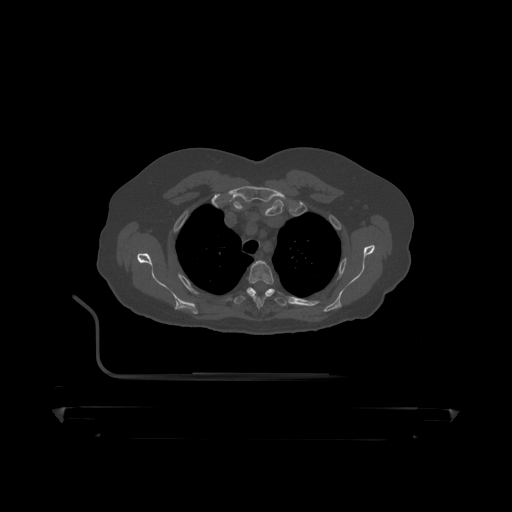
CT including the spine, one axial slice; position 352 of 390 along the scan axis; reconstruction kernel STANDARD; bone window (W 1800 / L 400 HU); 1.25 mm slice thickness; 512 × 512 image matrix. Patient: male, 60 years. Case-level facts recorded for this patient, not image findings: primary cancer: prostate.
Outlined on this slice (semi-automatically segmented with operator editing):
- T3 vertebra: bounding box <248,261,275,308> (left, top, right, bottom; pixels)
- T4 vertebra: <234,288,288,307>